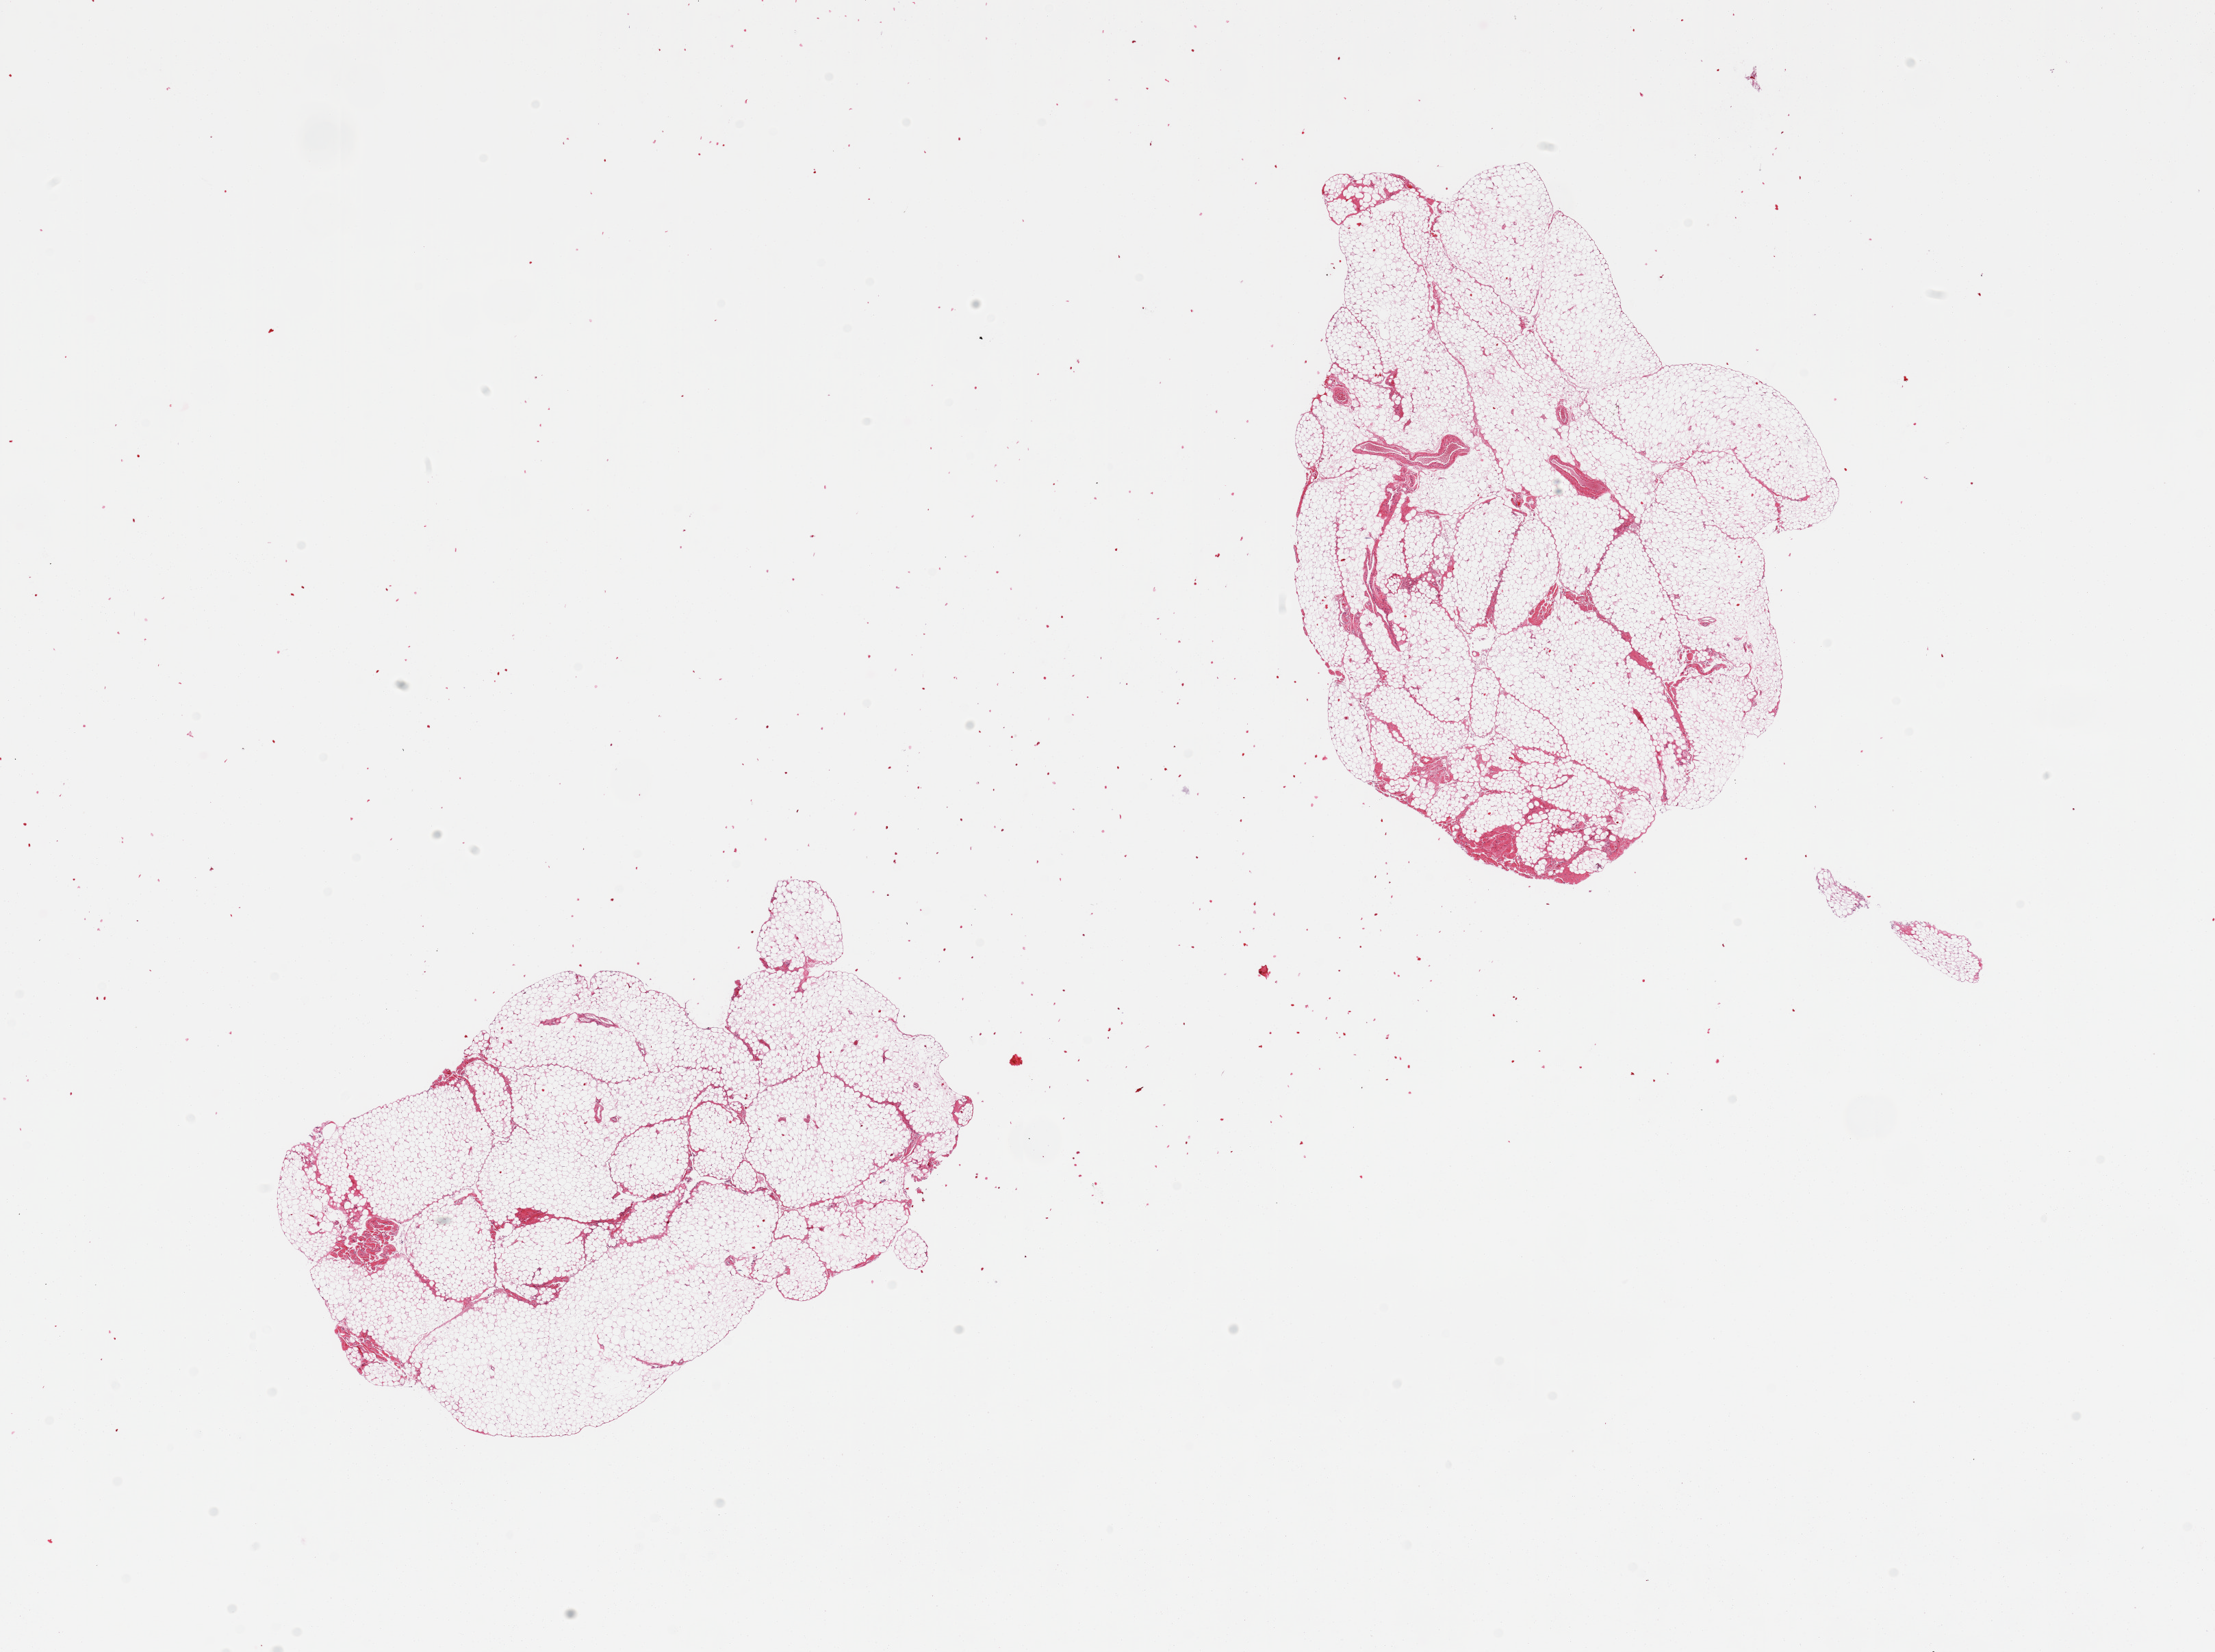
Digitized haematoxylin and eosin-stained section — a low-resolution overview of the entire scanned area, about 25.6 x 19.1 mm (acquisition: 20x scan), PAXgene-fixed paraffin-embedded (PFPE) section, sampled site (target tissue): adipose tissue, donor tissue sample.
• reviewer comment on this tissue sample: 2 pieces, adipose tissue (not pancreas as initially designated)